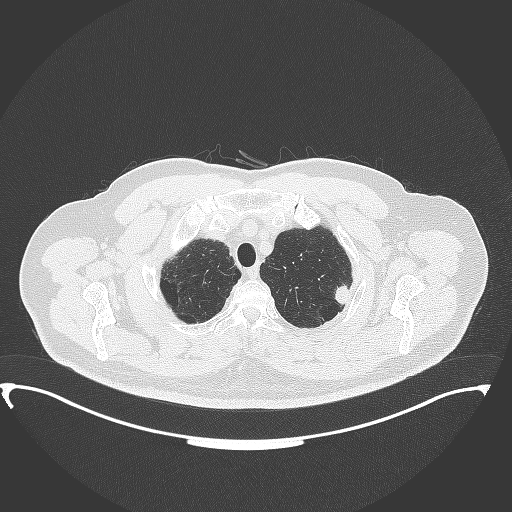
Chest CT, one axial slice. Slice 322 of 350 in the series (ordered by position). Reconstruction kernel B70f. 120 kVp. Lung window (W 1500 / L -600 HU). 1 mm slice thickness. 512 × 512 image matrix. Male patient, age 64 years. Case-level facts recorded for this patient, not image findings: clinical TNM (as recorded): T1c N1 M1.
Outlined on this slice (rectangle marked by the reading radiologist):
- lung tumour (recorded histology: adenocarcinoma): bounding box <332,280,352,308> (left, top, right, bottom; pixels)